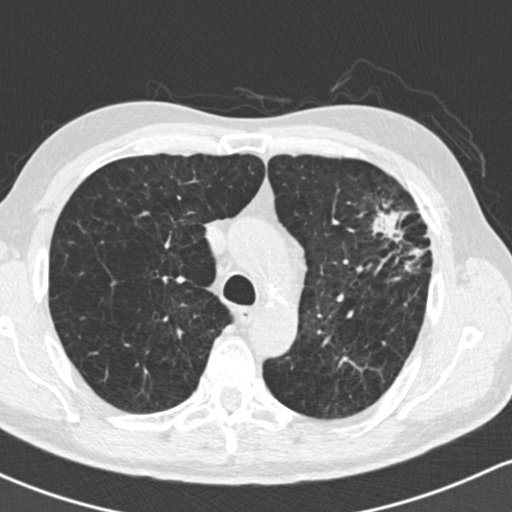
Low-dose screening chest CT, one axial slice; slice 111 of 162 in the series (ordered by position); reconstruction kernel B30f; 120 kVp; lung window (W 1500 / L -600 HU); 512 × 512 image matrix, field of view 318 × 318 mm.
Outlined on this slice (expert manual segmentation):
- lesion 1 (tumor, upper lobe of left lung): bounding box <372,211,425,272> (left, top, right, bottom; pixels)